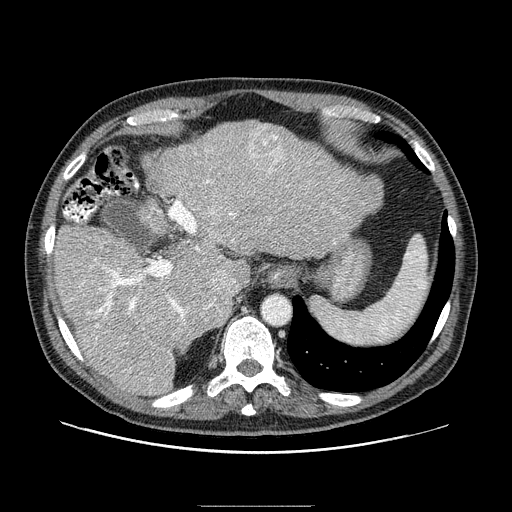
Contrast-enhanced abdominal CT (liver protocol), one axial slice; slice 62 of 99 in the series (ordered by position); 100 kVp; one of 2 acquisitions stored at this slice position; soft-tissue window (W 400 / L 40 HU); 512 × 512 image matrix, field of view 400 × 400 mm. From the clinical record (not read from this slice): diagnosis: hepatocellular carcinoma (patient treated with transarterial chemoembolisation; whether this scan precedes or follows treatment is not stated here); TNM stage (as recorded): Stage-II; Child-Pugh class: A; tumour differentiation: well differentiated; tumour size: 3.2 cm.
Annotated regions visible in this slice (semi-automatic segmentation, software-assisted and operator-edited):
- abdominal aorta: box from (x=263, y=296) to (x=291, y=324) px
- liver parenchyma outside the tumour (the mass and vessels are separate outlines, so this box may not span the whole liver): (x=54, y=121)–(x=382, y=394)
- mass: (x=249, y=127)–(x=285, y=175)
- liver vessels: (x=71, y=149)–(x=288, y=381)